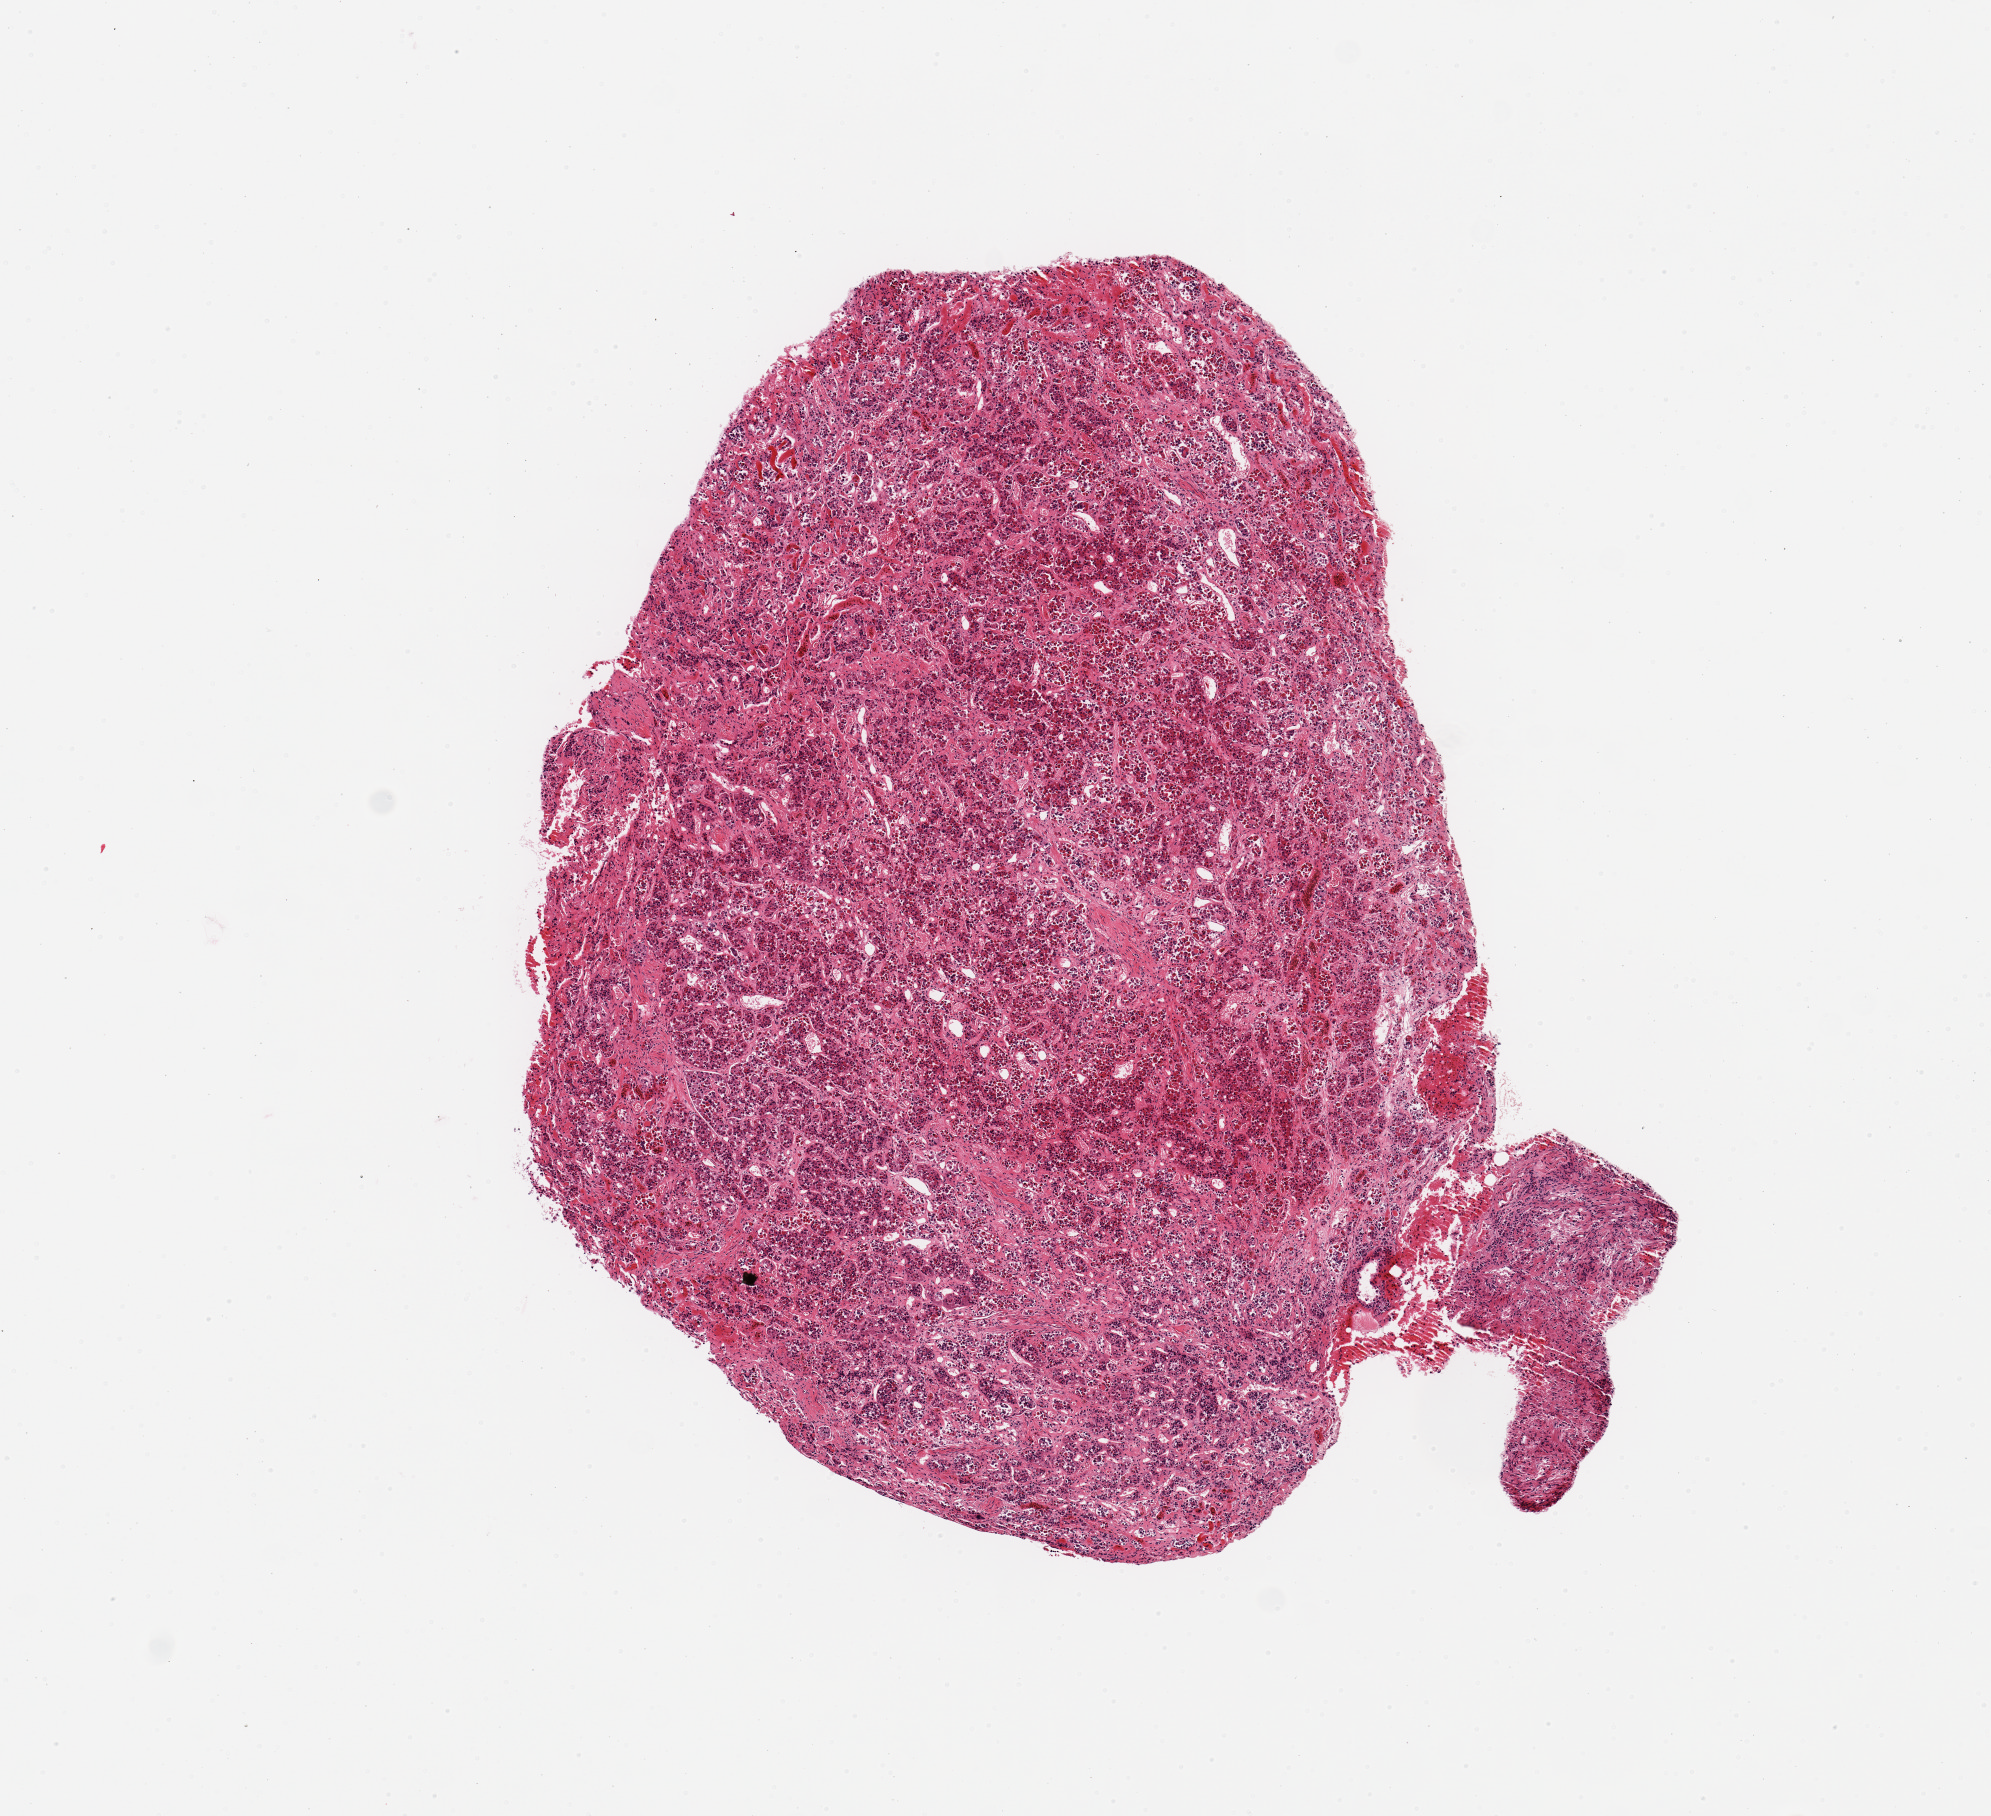
Whole-slide image, hematoxylin and eosin (H&E) stain, a low-resolution overview of the entire scanned area, about 7.9 x 7.2 mm (acquisition: 20x scan); PAXgene-fixed, paraffin-embedded tissue; section of pituitary (target tissue); donor tissue sample. Donor sex: male.
Review note (as recorded): 1 piece; mostly adenohypophysis.